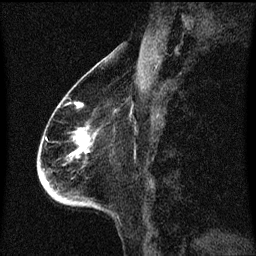
Breast MRI (dynamic contrast-enhanced), one sagittal slice. Dynamic contrast-enhanced series, image 2 of 3 at this slice position (ordered by acquisition). 1.5 T. TE 4.2 ms, TR 8.4 ms. 2 mm slice thickness. 256 × 256 image matrix, field of view 200 × 200 mm. Patient: female, 68 years. From the clinical record (not read from this slice): setting: breast cancer imaged before/during neoadjuvant chemotherapy; receptor status: triple-negative.
Outlined on this slice (semi-automatically segmented with operator editing):
- analysis volume of interest (the breast-tissue region the enhancement analysis was run in; not a lesion): bounding box <40,96,107,209> (left, top, right, bottom; pixels)
- tumour enhancement mask (voxels above the 70 % enhancement threshold inside the analysis volume of interest): <73,102,93,155>